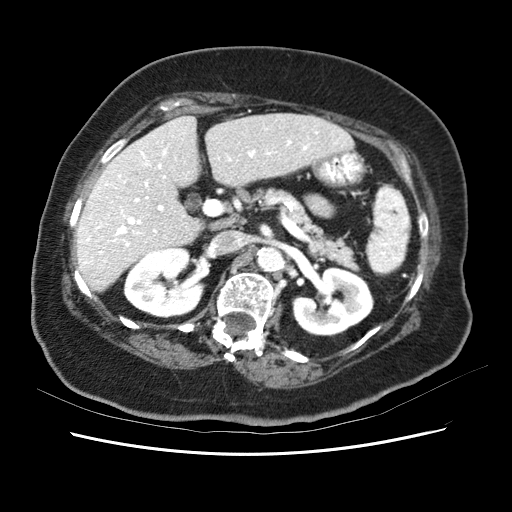
Contrast-enhanced abdominal CT (liver protocol), one axial slice; slice 29 of 62 in the series (ordered by position); soft-tissue window (W 400 / L 40 HU); 2.5 mm slice thickness; 512 × 512 image matrix. Case-level facts recorded for this patient, not image findings: diagnosis: hepatocellular carcinoma (patient treated with transarterial chemoembolisation; whether this scan precedes or follows treatment is not stated here); TNM stage (as recorded): Stage-I; Child-Pugh class: B; tumour size: 5.3 cm.
Outlined on this slice (semi-automatic segmentation, software-assisted and operator-edited):
- liver parenchyma outside the tumour (the mass and vessels are separate outlines, so this box may not span the whole liver): bounding box [x1, y1, x2, y2] px = [76, 112, 356, 294]
- liver vessels: [79, 116, 343, 272]